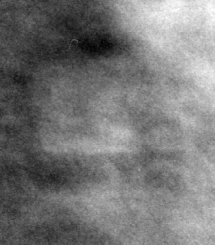
Cropped region of a digitized screen-film mammogram centred on a radiologist-marked abnormality, left breast, MLO view.
Finding: mass, shape lobulated, margins circumscribed; BI-RADS assessment category 4; pathology (as recorded): benign.